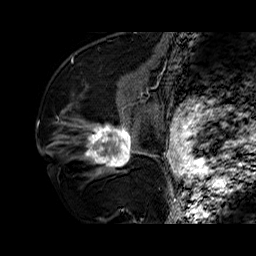
Breast MRI (dynamic contrast-enhanced), one sagittal slice. Slice 35 of 60 in the series (ordered by position). Dynamic contrast-enhanced series, time point 2 of 6 at this slice position (early post-contrast). 1.5 T. TE 6.4 ms, TR 32.7 ms. 256 × 256 image matrix, field of view 200 × 200 mm. Female patient. Case-level facts recorded for this patient, not image findings: setting: breast cancer imaged before/during neoadjuvant chemotherapy; receptor status: HR-positive, HER2-negative.
Outlined on this slice (semi-automatic segmentation, software-assisted and operator-edited):
- analysis volume of interest (the breast-tissue region the enhancement analysis was run in; not a lesion): box from (x=73, y=110) to (x=141, y=179) px
- tumour enhancement mask (voxels above the 100 % enhancement threshold inside the analysis volume of interest): (x=85, y=125)–(x=137, y=171)